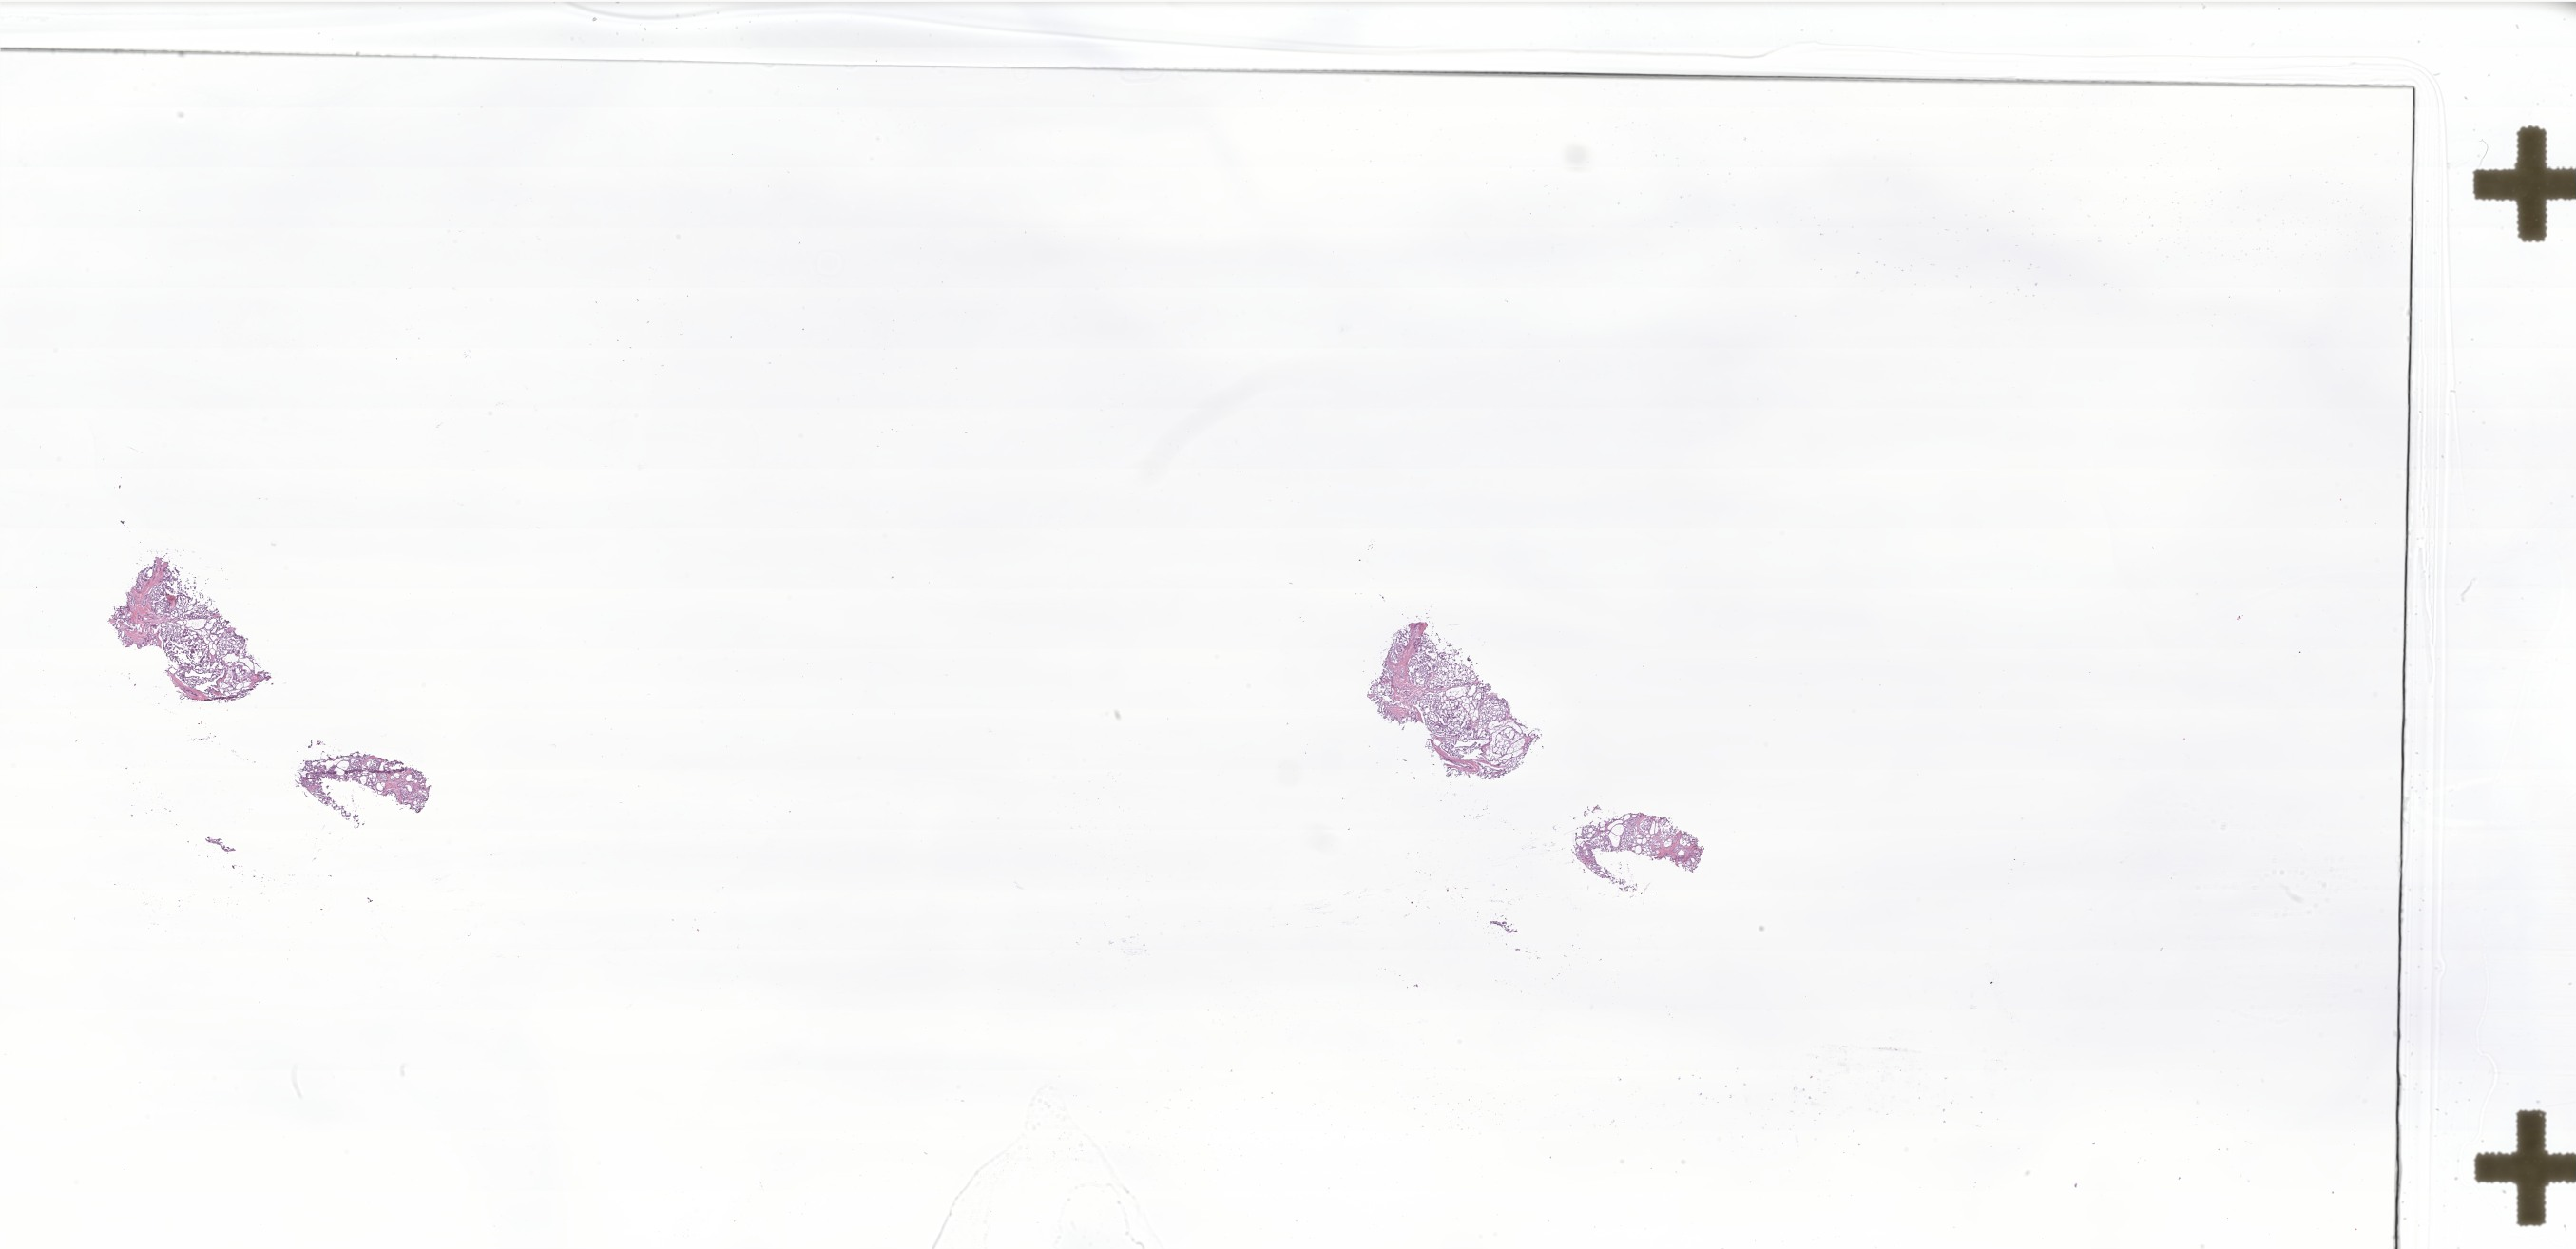
Whole-slide image, H&E stain of tumor tissue from the thyroid, a low-resolution overview of the entire scanned area, about 45.7 x 22.2 mm; frozen section. Patient female; age 157 months.
- diagnosis: Papillary carcinoma, follicular variant